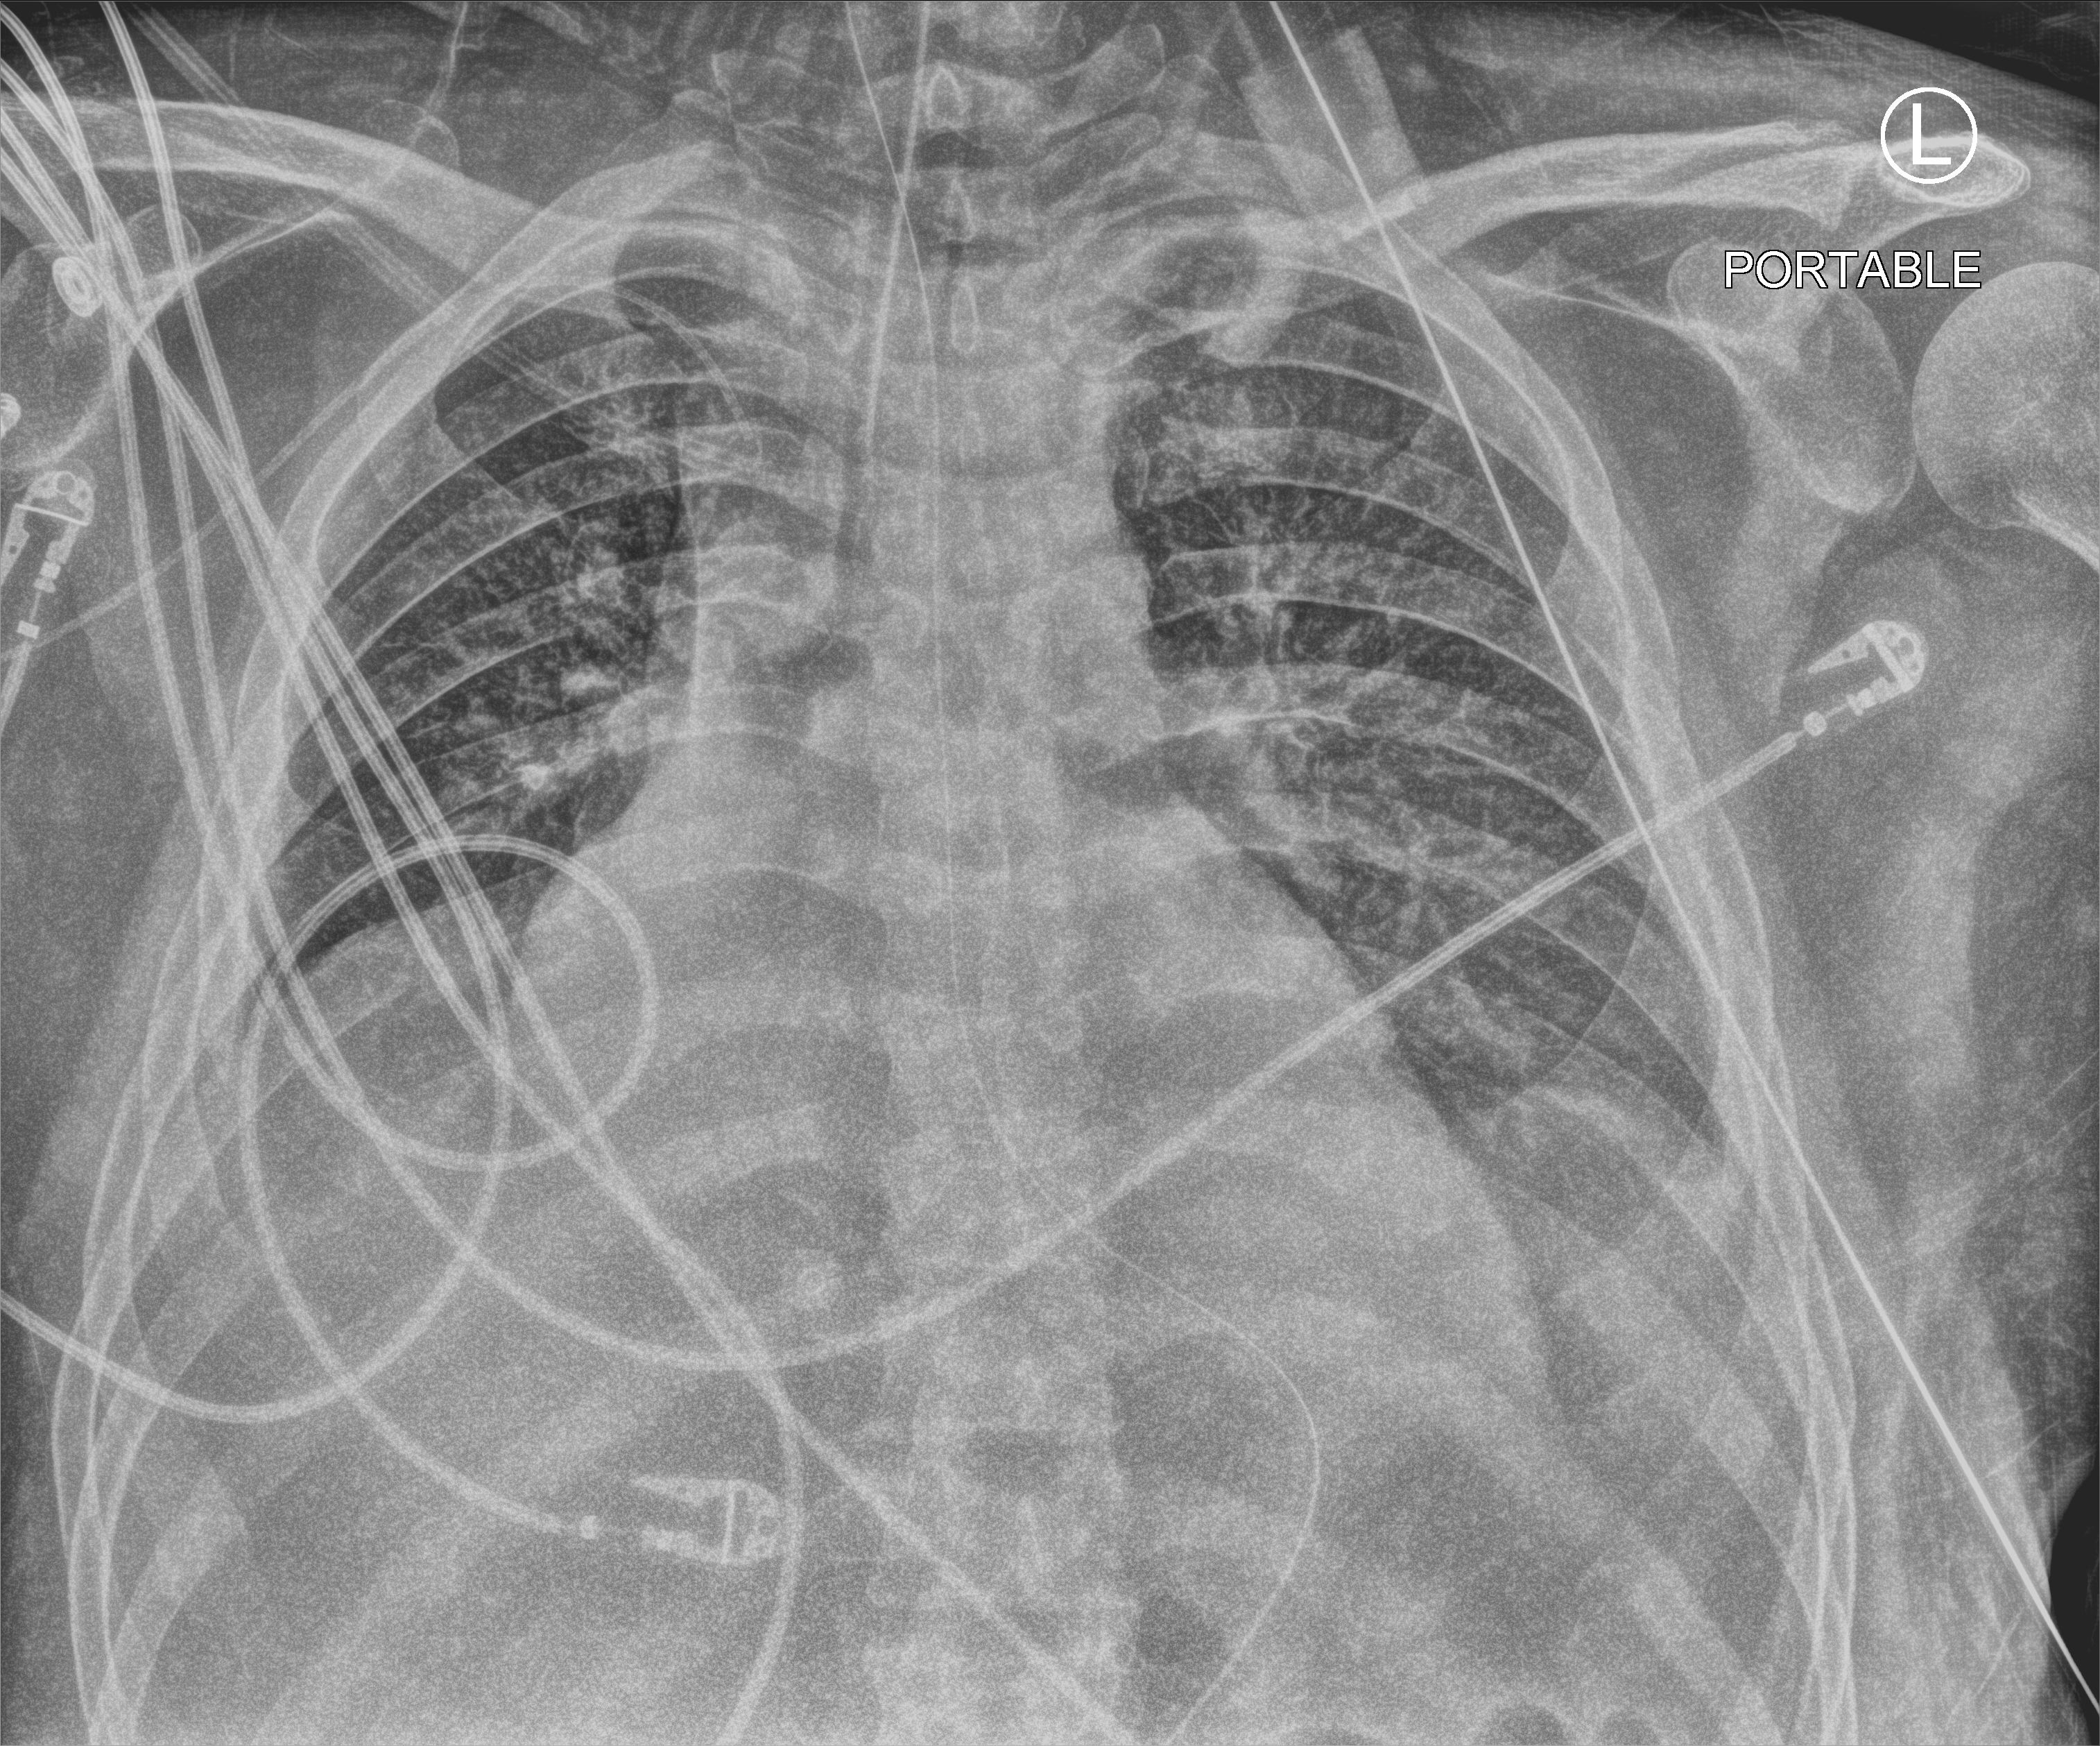
Portable chest radiograph, anteroposterior (AP) projection. Patient hospitalised with COVID-19; male, aged 18–59 years.
Admission-level facts for this patient (not findings on this image; timing relative to this image not recorded):
- mechanically ventilated during this hospital stay: yes
- admitted to intensive care during this hospital stay: yes